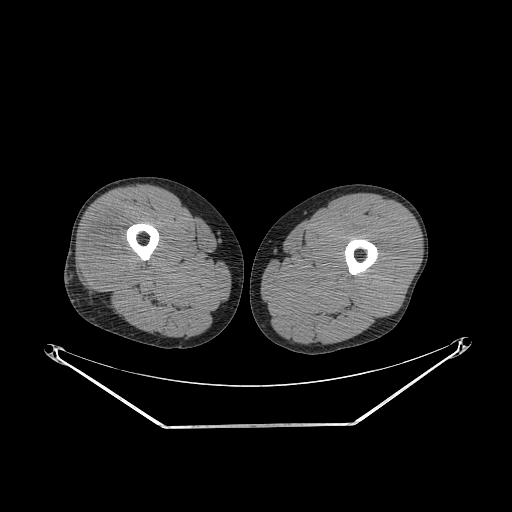
CT of an extremity soft-tissue mass (from a PET/CT study), one axial slice; position 235 of 267 along the scan axis; soft-tissue window (W 400 / L 40 HU); 3.75 mm slice thickness; 512 × 512 image matrix, field of view 500 × 500 mm. Male patient. Case-level facts recorded for this patient, not image findings: histological type: poorly differentiated synovial sarcoma; grade: high; site of the primary tumour: right buttock.
Outlined on this slice (expert contour drawn on MRI and transferred to this co-registered scan by the dataset authors):
- gross tumour volume including surrounding oedema: box from (x=84, y=219) to (x=131, y=287) px
- gross tumour volume (mass): (x=85, y=228)–(x=131, y=286)